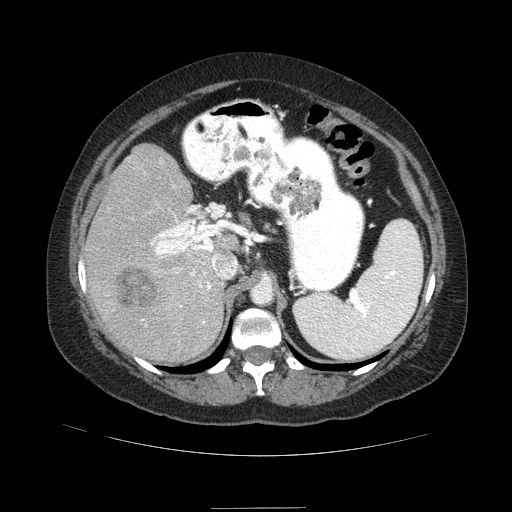
Contrast-enhanced abdominal CT (liver protocol), one axial slice. Slice 54 of 89 in the series (ordered by position). Reconstruction kernel STANDARD. Soft-tissue window (W 400 / L 40 HU). 2.5 mm slice thickness. 512 × 512 image matrix, field of view 400 × 400 mm. From the clinical record (not read from this slice): diagnosis: hepatocellular carcinoma (patient treated with transarterial chemoembolisation; whether this scan precedes or follows treatment is not stated here); TNM stage (as recorded): Stage-IIIB; Child-Pugh class: A; tumour nodularity: multinodular.
Outlined on this slice (semi-automatic segmentation, software-assisted and operator-edited):
- liver parenchyma outside the tumour (the mass and vessels are separate outlines, so this box may not span the whole liver): bounding box (x1, y1, x2, y2) in pixels: (84, 144, 238, 362)
- mass: (117, 267, 158, 312)
- liver vessels: (142, 186, 234, 324)